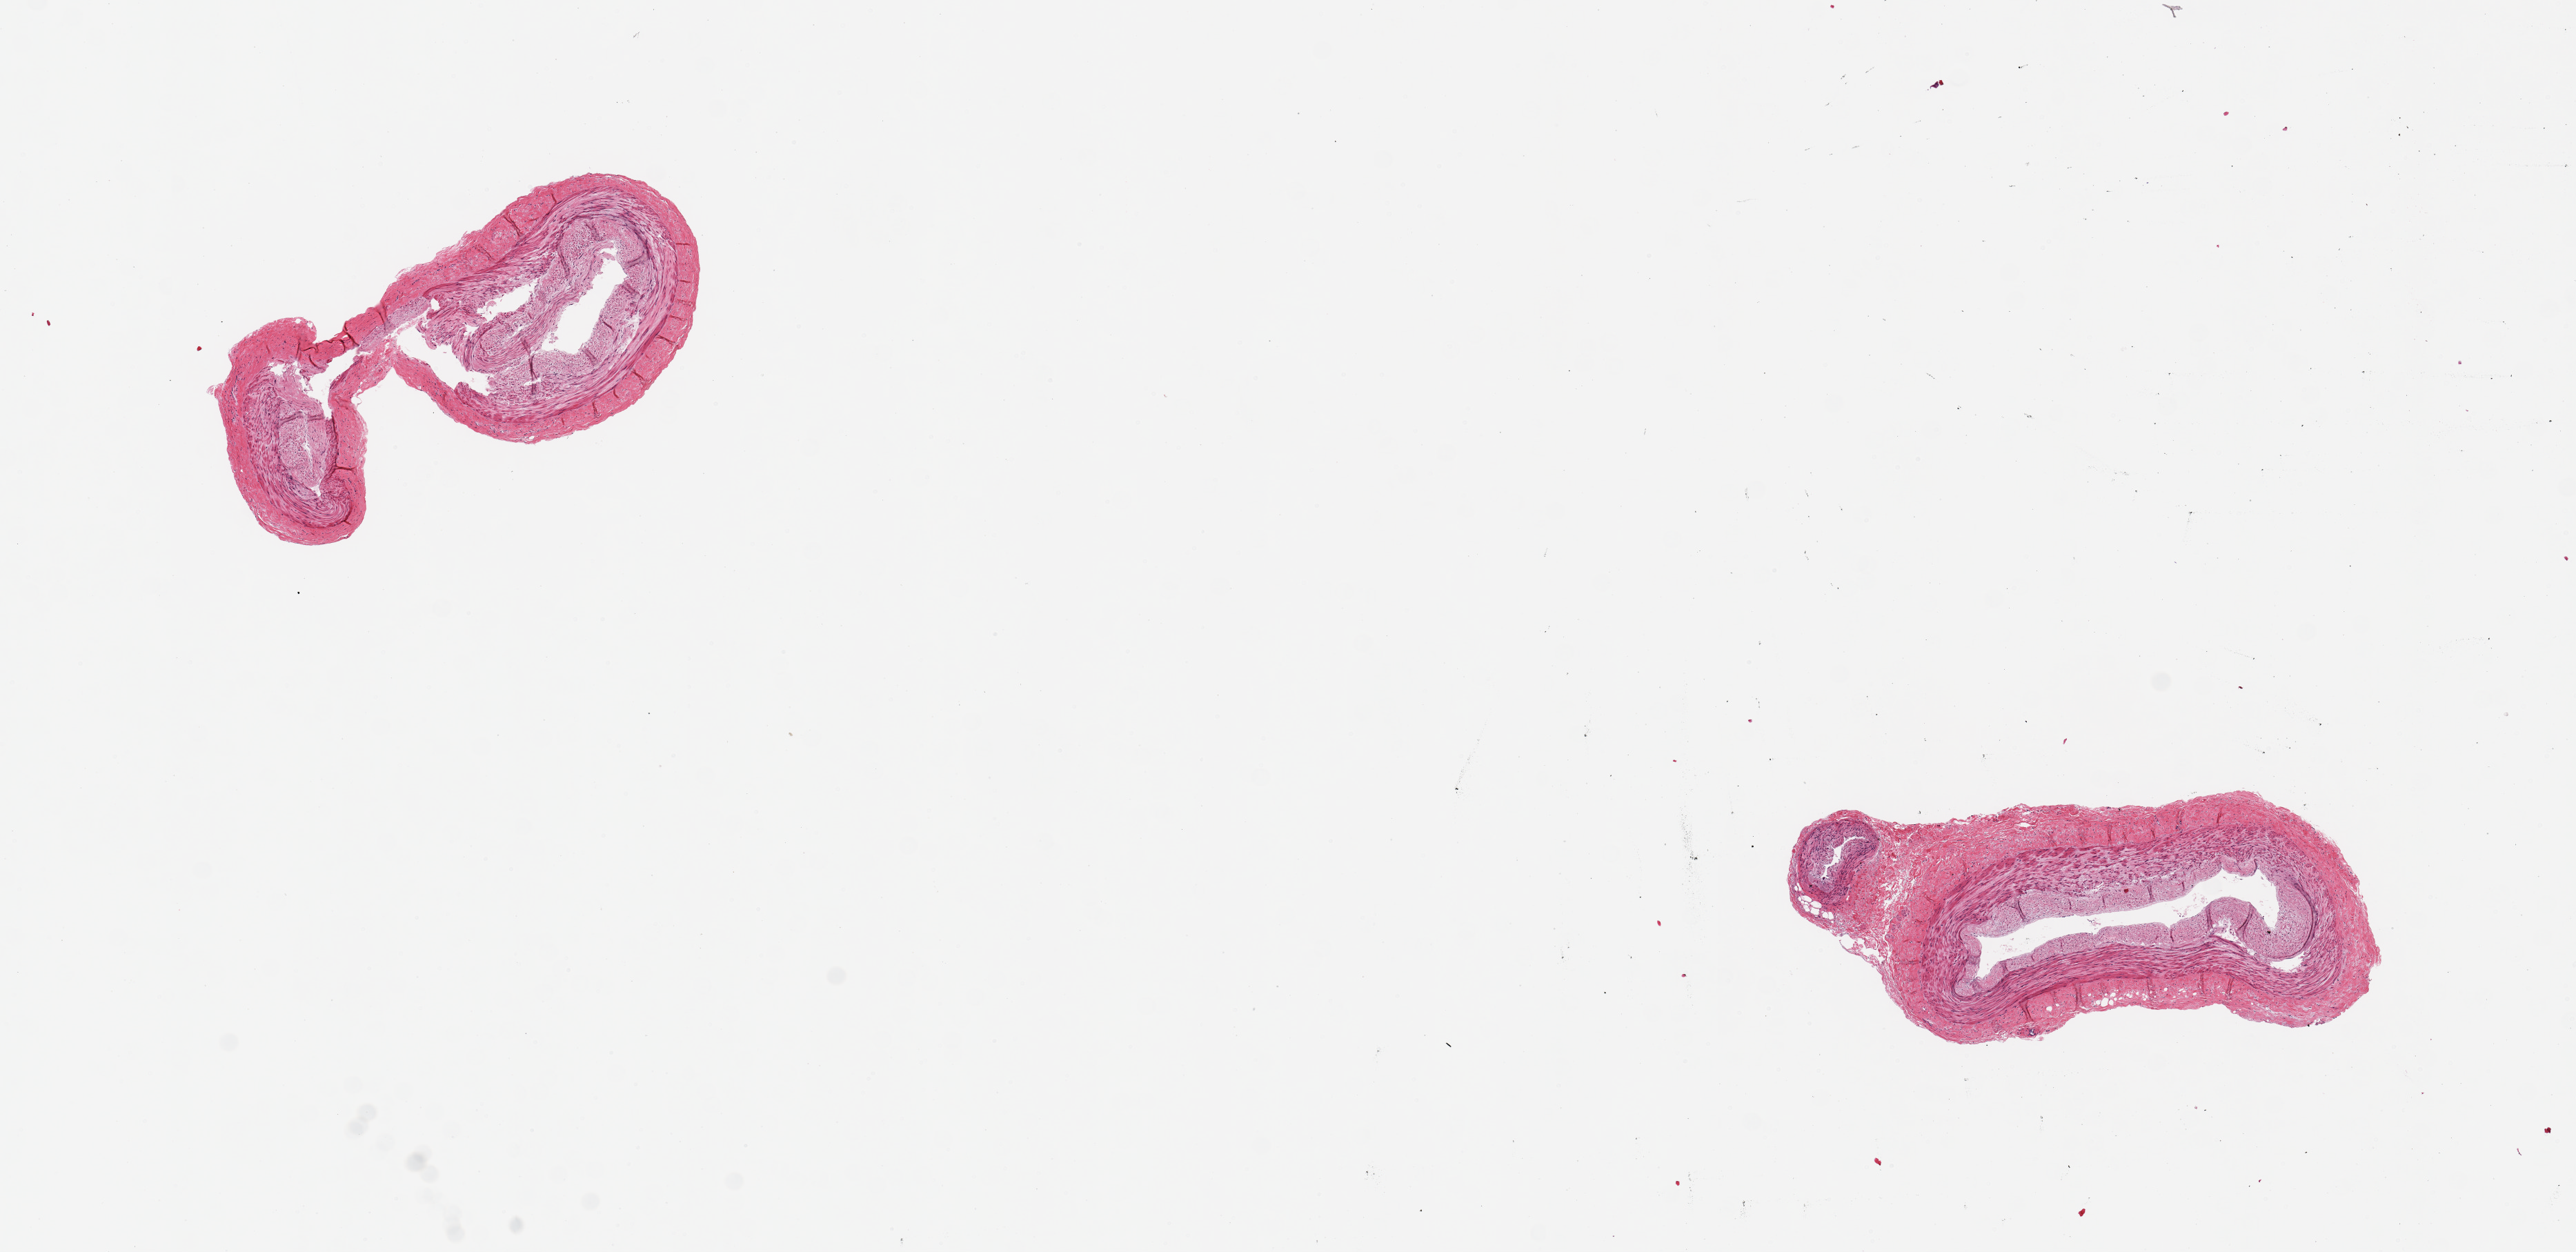
Hematoxylin and eosin (H&E) whole-slide image, low-resolution overview of the scanned area, about 14.8 x 7.2 mm, PAXgene-fixed paraffin-embedded (PFPE) section, section of tibial artery (target tissue), donor tissue sample.
- review note (as recorded): 2 pieces, 3x1 & 3x1mm; well trimmed but with tissue fracture artifacts